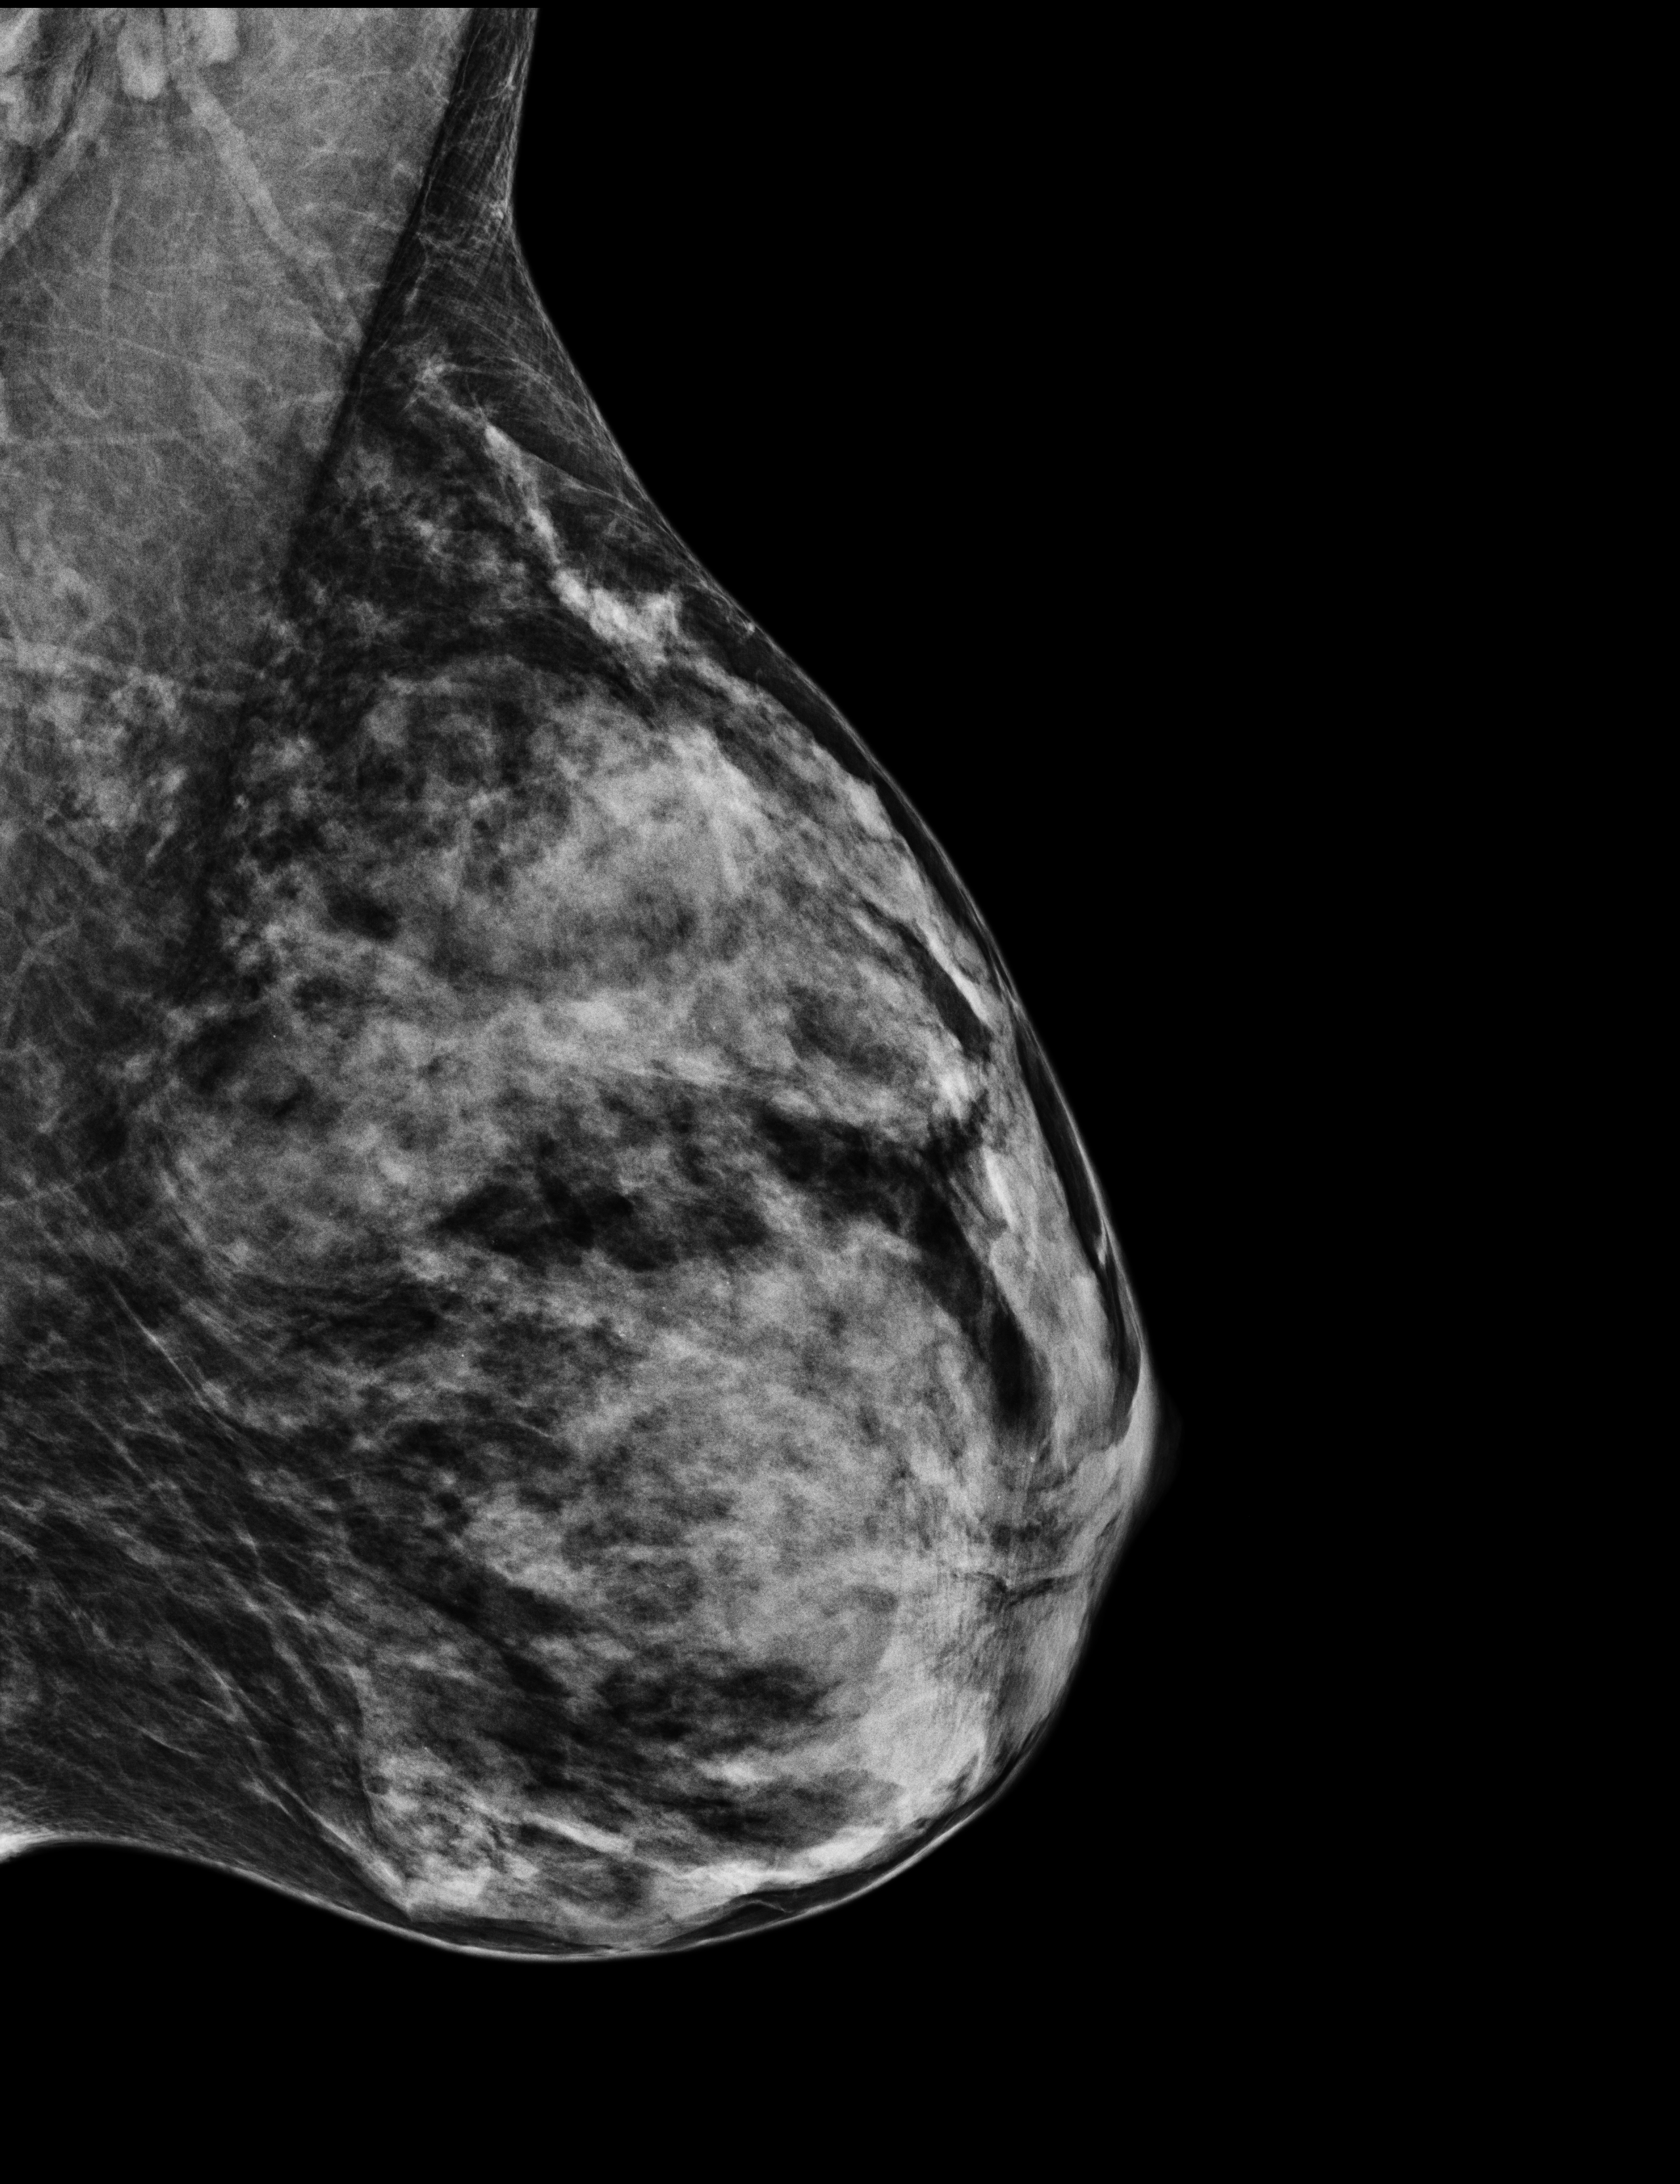
Full-field digital mammogram (FFDM), left breast, mediolateral oblique (MLO) view, annual screening mammography examination, system: Selenia Dimensions. Female patient, age 43 years.
BI-RADS breast density category at the screening exam (both breasts, scale 1–4): 4. Final BI-RADS assessment for this screening round (tomosynthesis exam, both breasts): category 2. Recall: no recall after this screen.